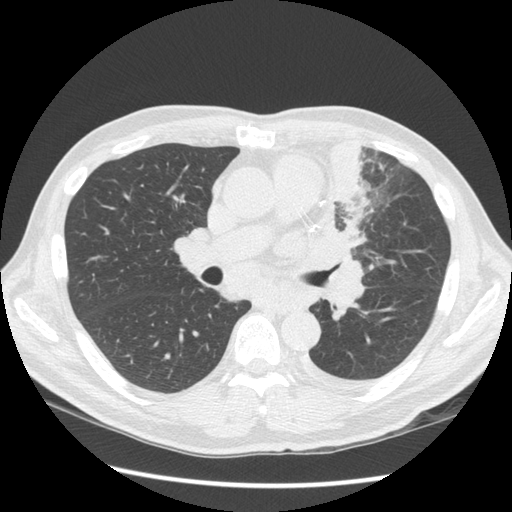
Low-dose screening chest CT, one axial slice; position 81 of 136 along the scan axis; lung window (W 1500 / L -600 HU); 2.5 mm slice thickness; 512 × 512 image matrix, field of view 360 × 360 mm.
Outlined on this slice (expert manual segmentation):
- lesion 1 (tumor, upper lobe of left lung): bounding box (x1, y1, x2, y2) in pixels: (318, 141, 374, 267)